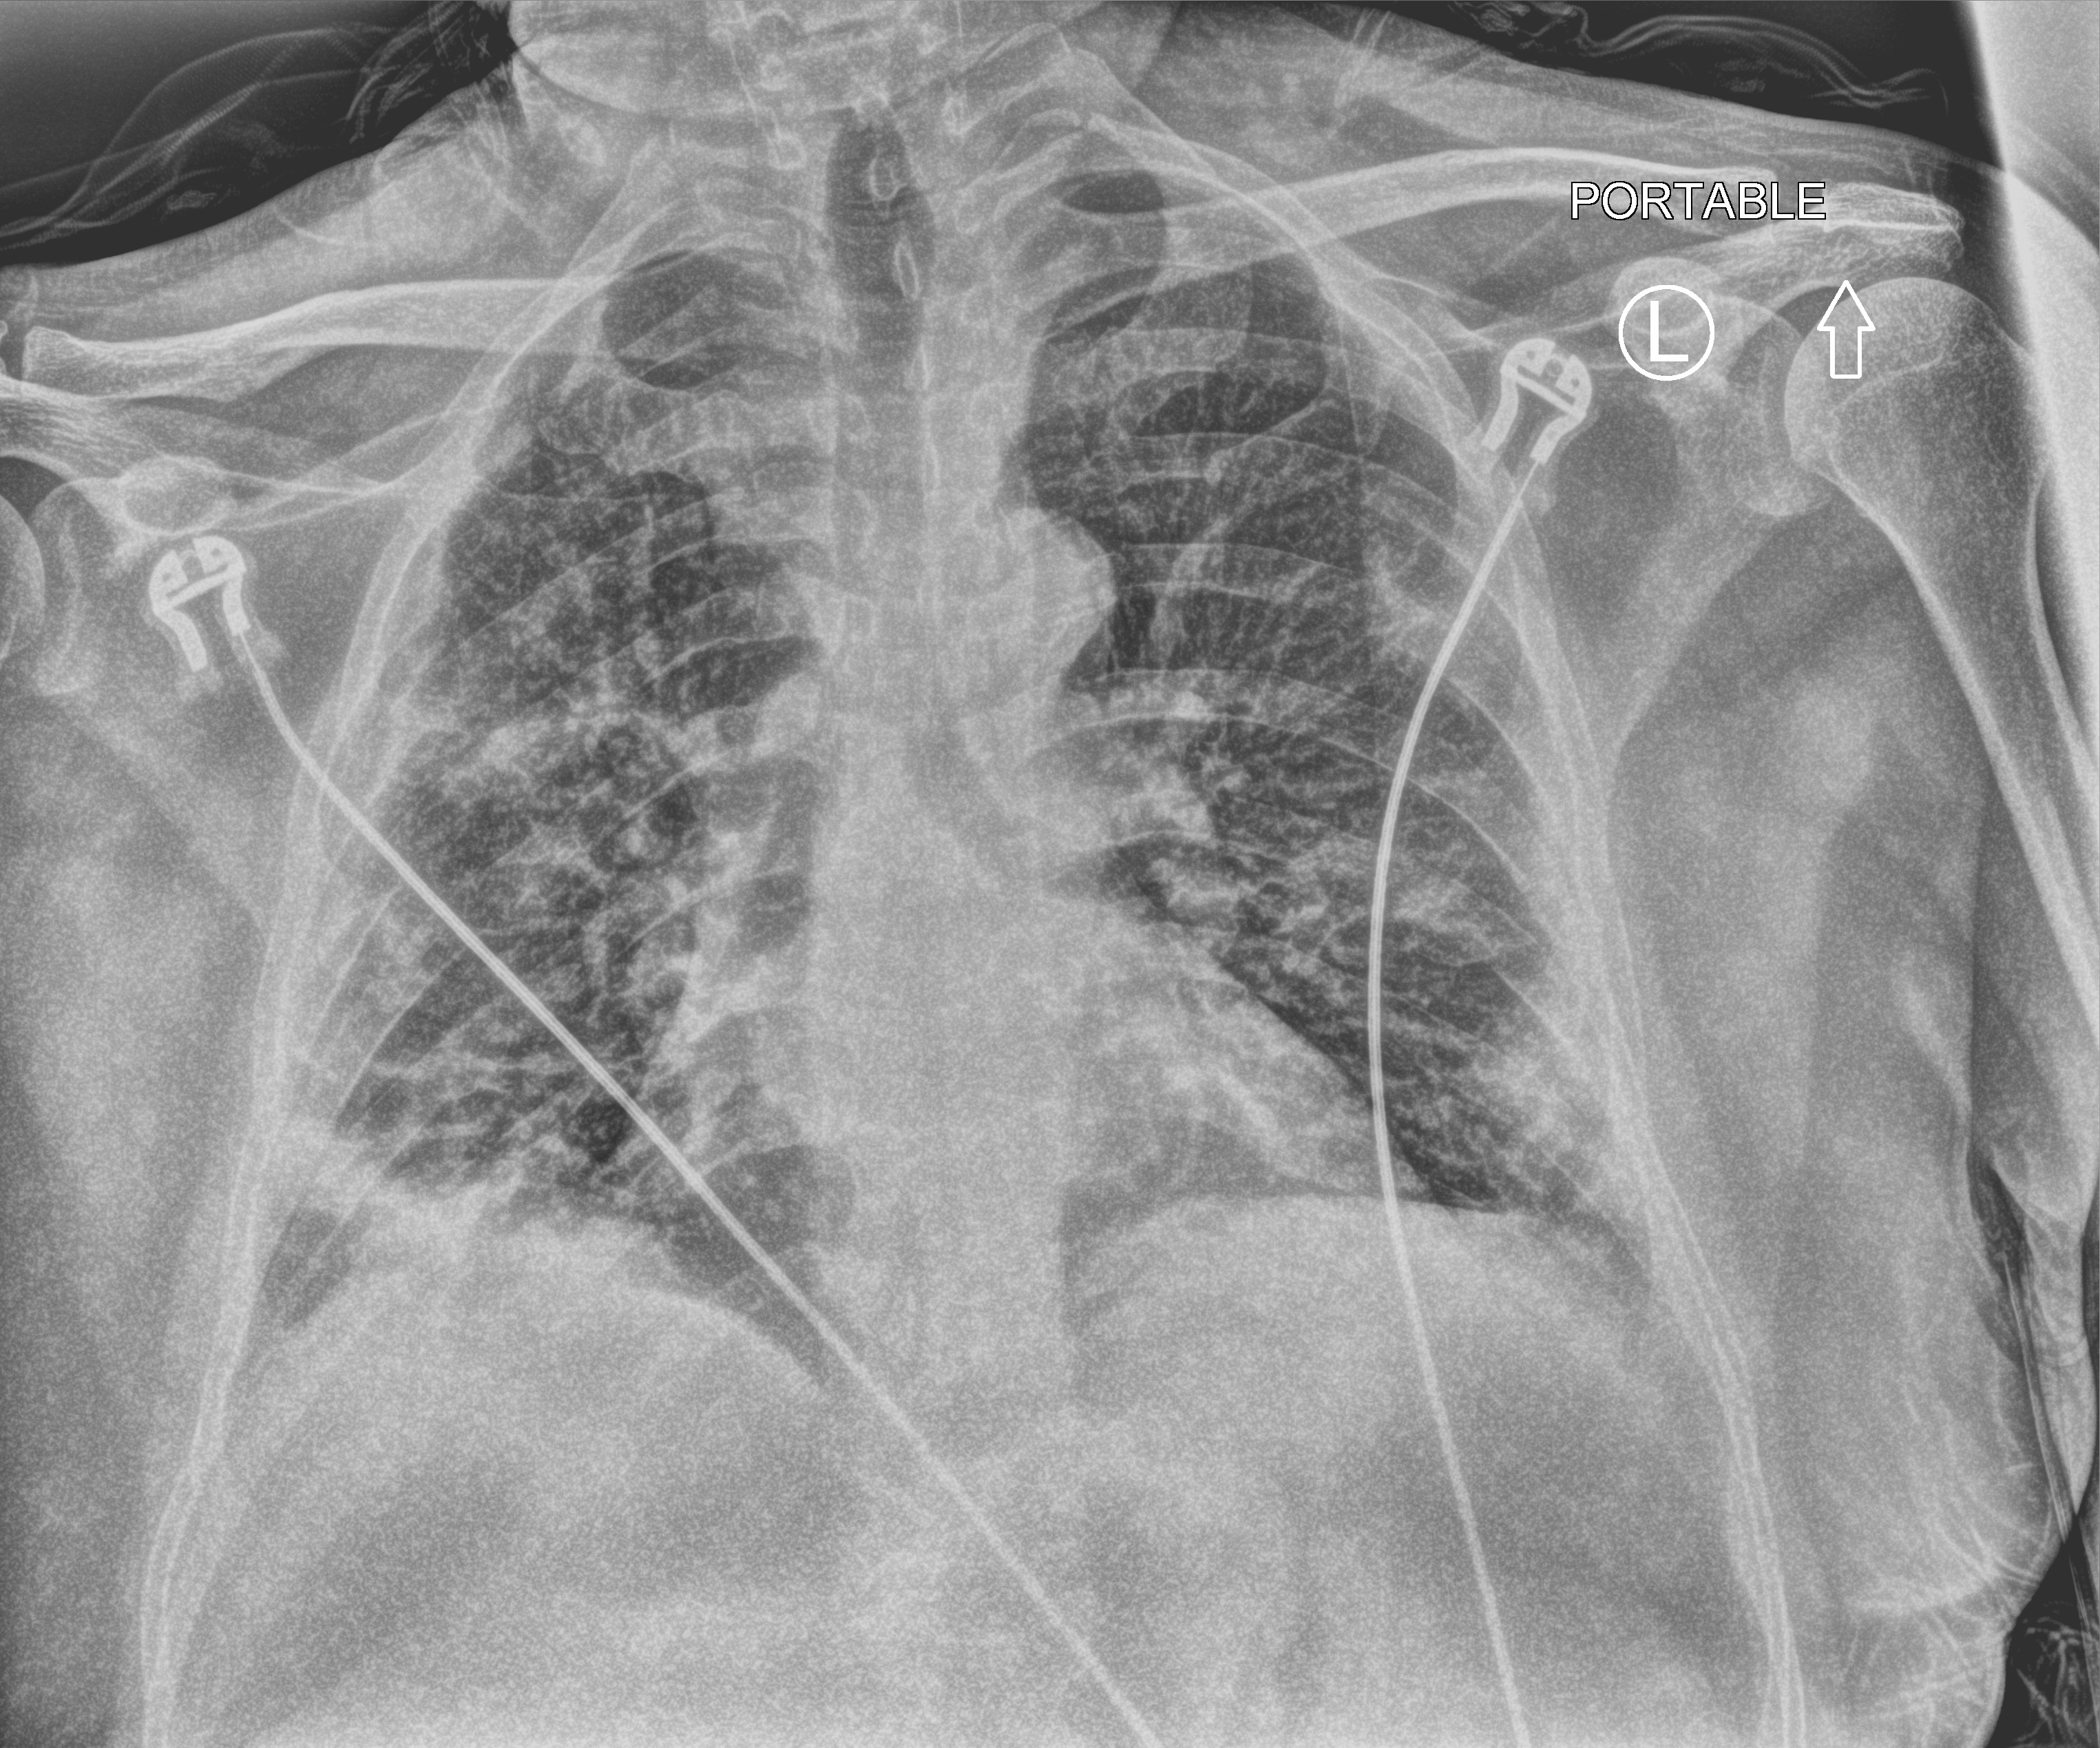
Portable chest radiograph; anteroposterior (AP) projection. Patient hospitalised with COVID-19; male, aged 60–74 years.
Admission-level facts for this patient (not findings on this image; timing relative to this image not recorded):
- length of hospital stay: 5 days
- admitted to intensive care during this hospital stay: yes
- mechanically ventilated during this hospital stay: no